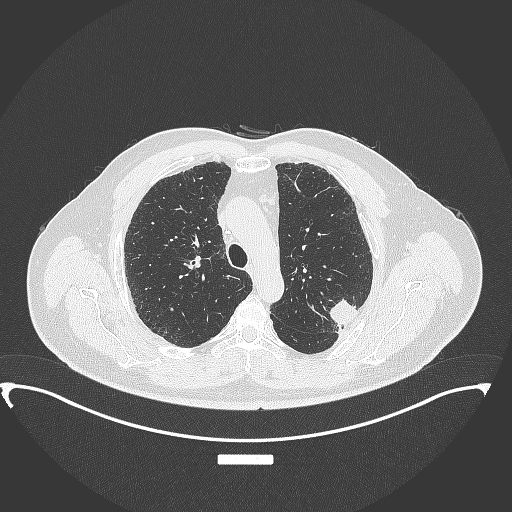
Chest CT, one axial slice; slice 263 of 350 in the series (ordered by position); reconstruction kernel B70f; lung window (W 1500 / L -600 HU); 512 × 512 image matrix, field of view 459 × 459 mm. Male patient, age 64 years. From the clinical record (not read from this slice): clinical TNM (as recorded): T1c N1 M1.
Structures marked on this image (rectangle marked by the reading radiologist):
- lung tumour (recorded histology: adenocarcinoma): bounding box [x1, y1, x2, y2] px = [327, 293, 363, 331]